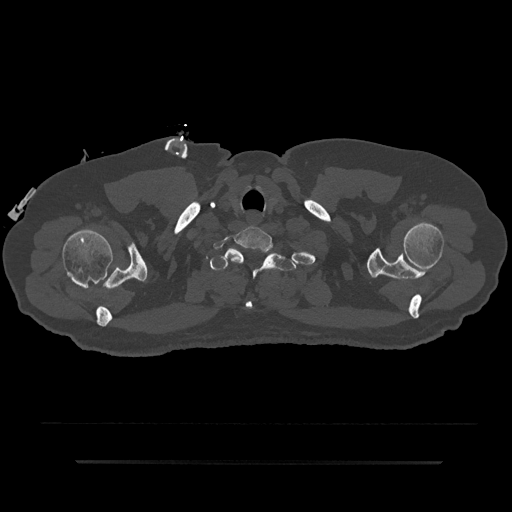
CT including the spine, one axial slice; slice 753 of 797 in the series (ordered by position); reconstruction kernel Br40s/3; 120 kVp; bone window (W 1800 / L 400 HU); 0.5 mm slice thickness; 512 × 512 image matrix, field of view 464 × 464 mm. Patient: male, 59 years. From the clinical record (not read from this slice): primary cancer: bile ducts; vertebrae with lytic lesions (as recorded): T10.
Outlined on this slice (semi-automatic segmentation, software-assisted and operator-edited):
- T1 vertebra: bounding box (x1, y1, x2, y2) in pixels: (210, 249, 296, 309)